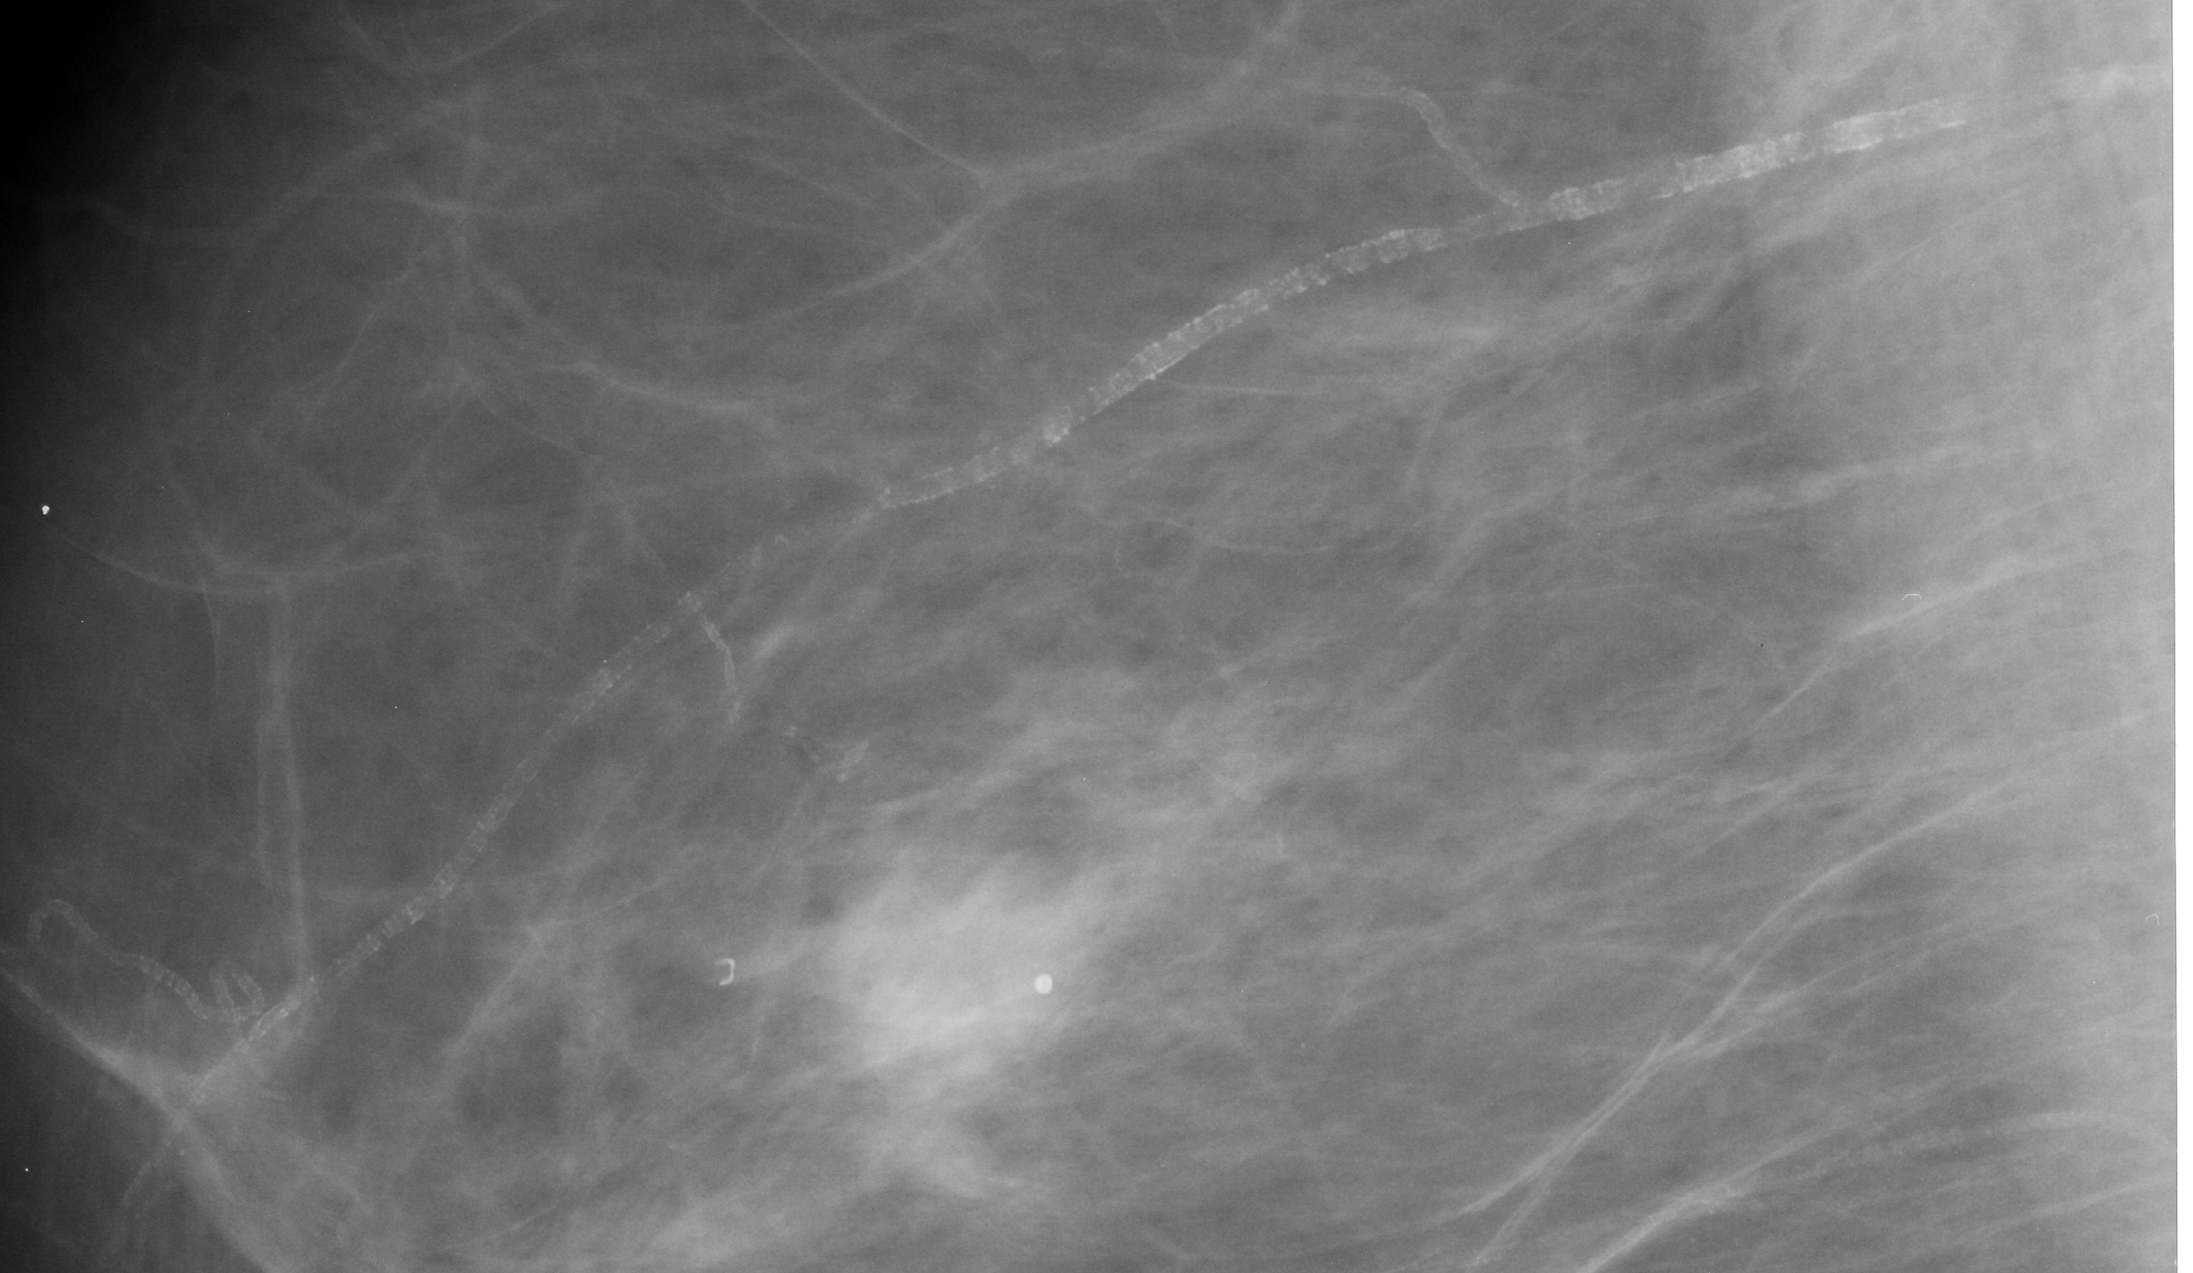
Cropped region of a digitized screen-film mammogram centred on a radiologist-marked abnormality, right breast, MLO view, BI-RADS breast density category 2 (scale 1–4).
Calcifications, morphology vascular; BI-RADS assessment category 2; subtlety rating 5 on a 1 (subtle) to 5 (obvious) scale; benign without callback (not worked up further).